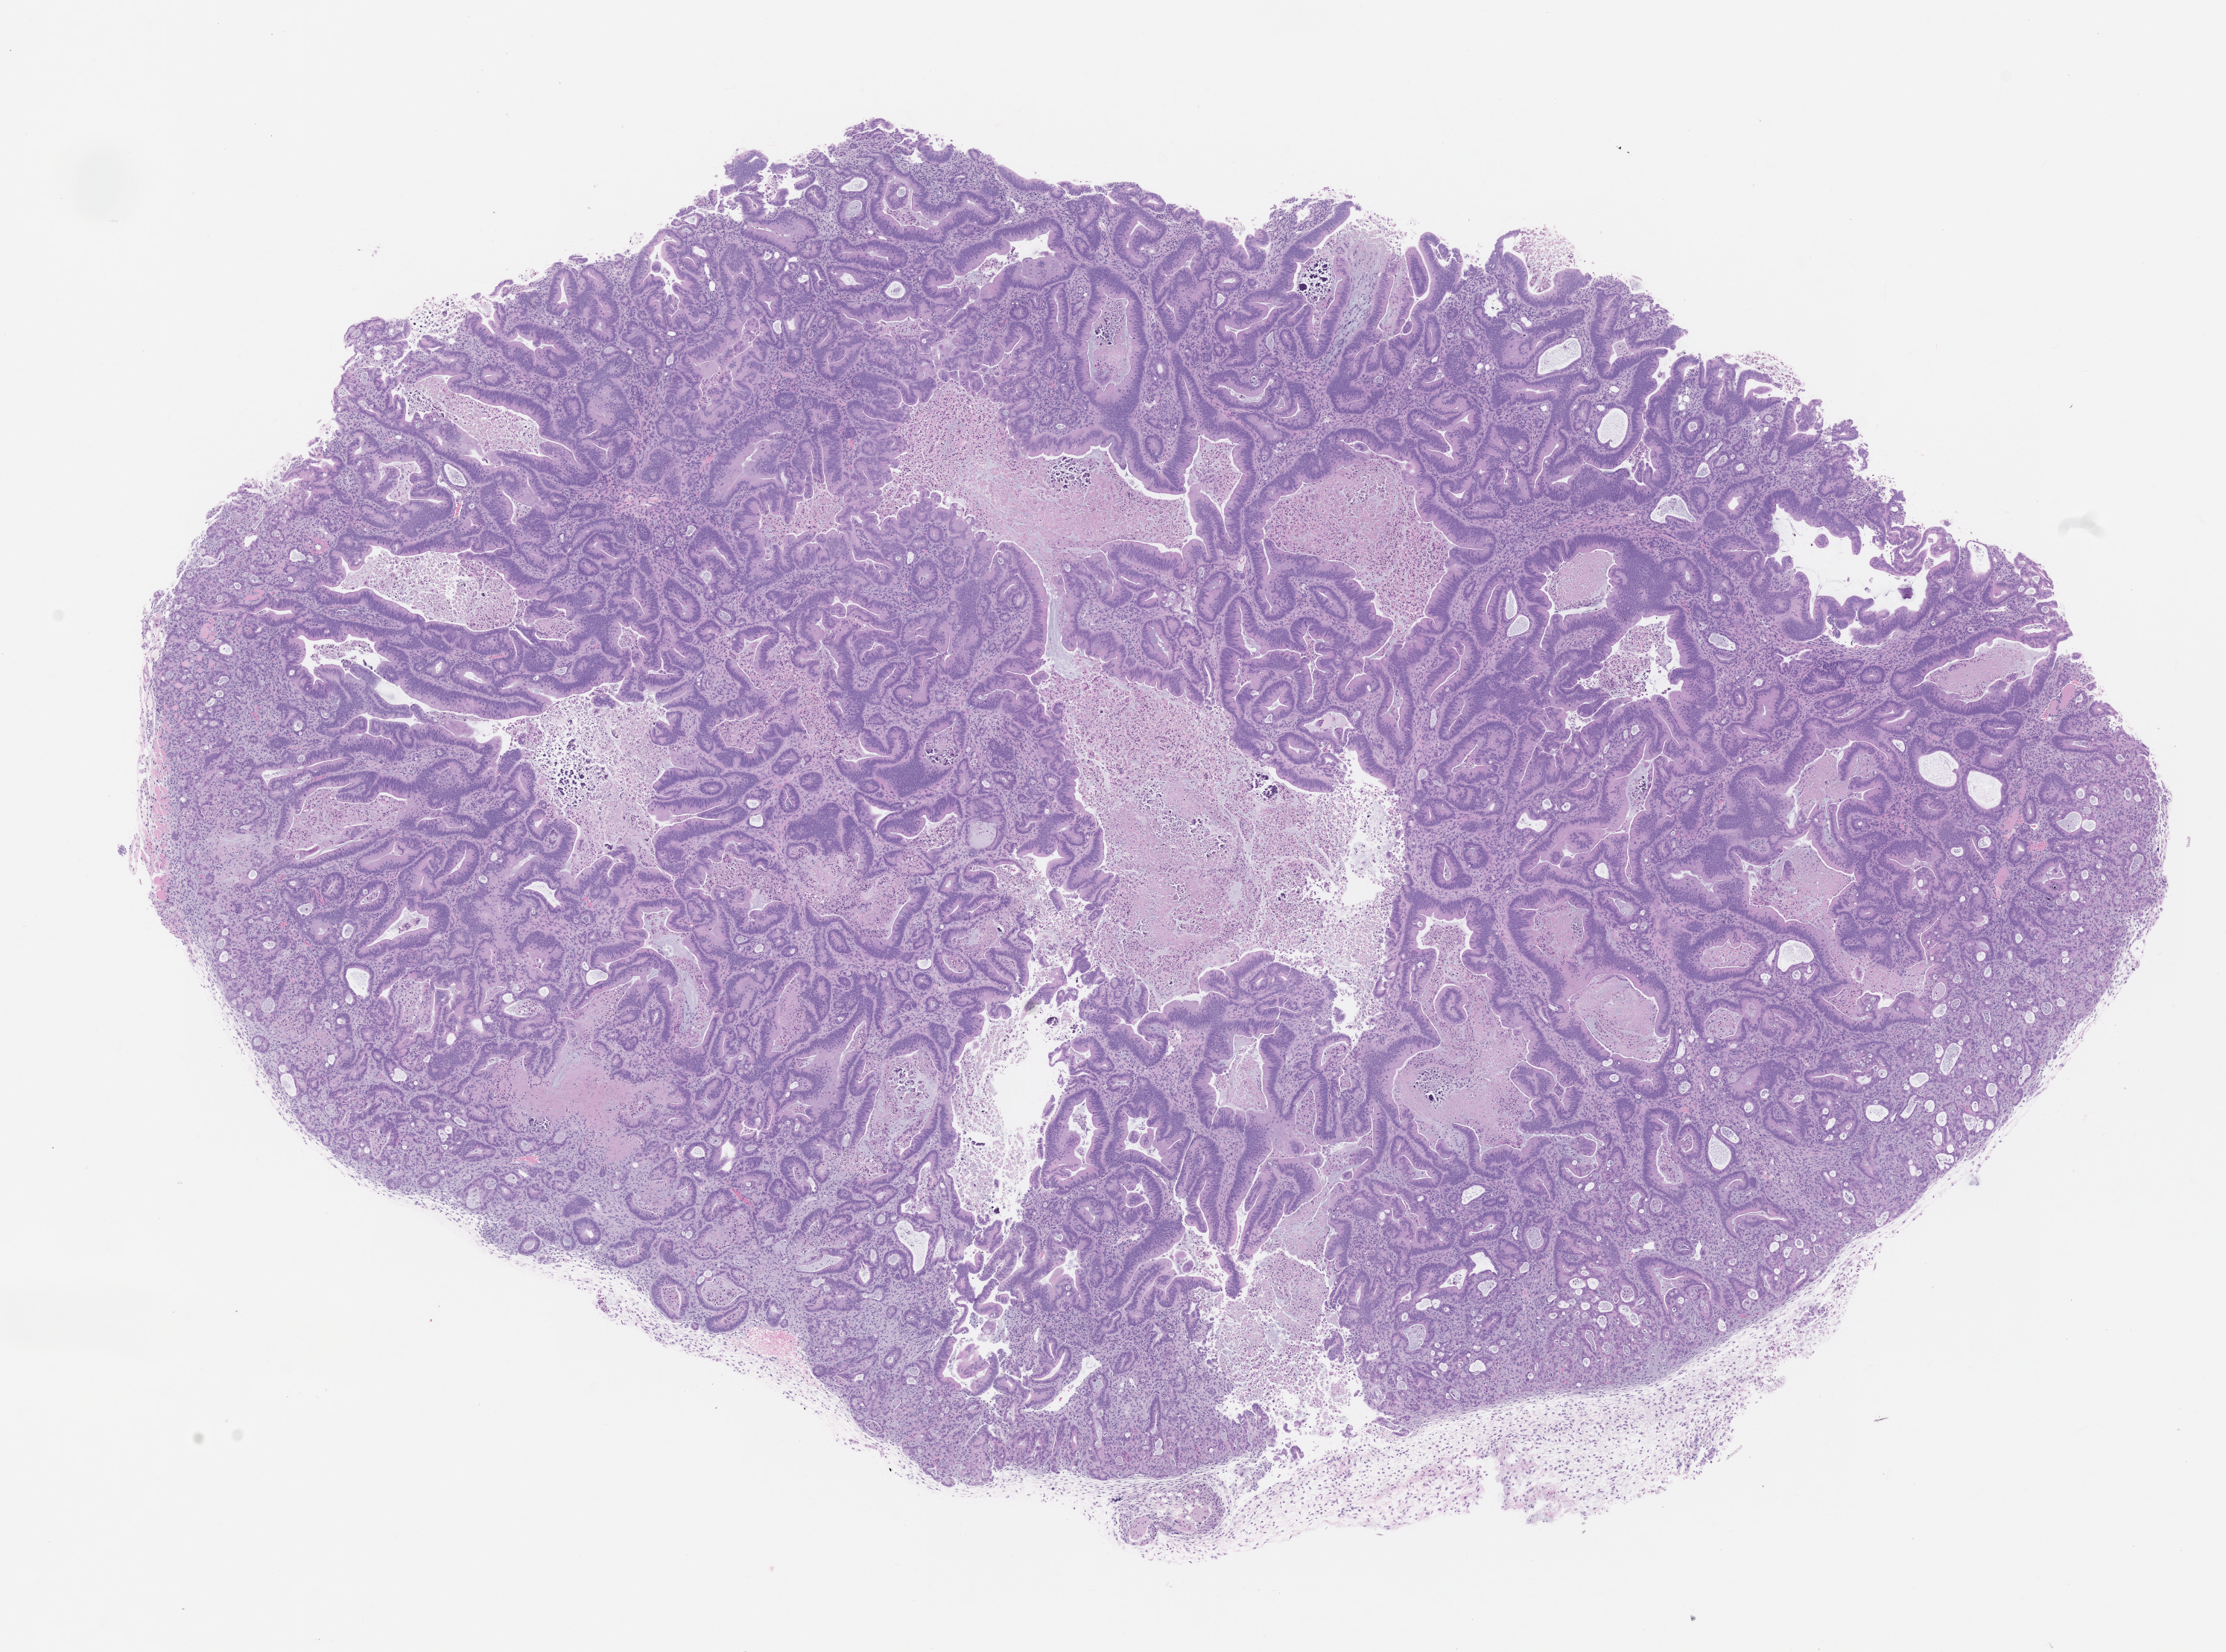
Whole-slide image, haematoxylin and eosin: patient-derived xenograft (human tumor grown in a mouse), passage 1, low-resolution overview of the scanned area, about 12.0 x 8.9 mm; FFPE section; tumor site category: colon.
Originating patient diagnosis: Colon Adenocarcinoma.